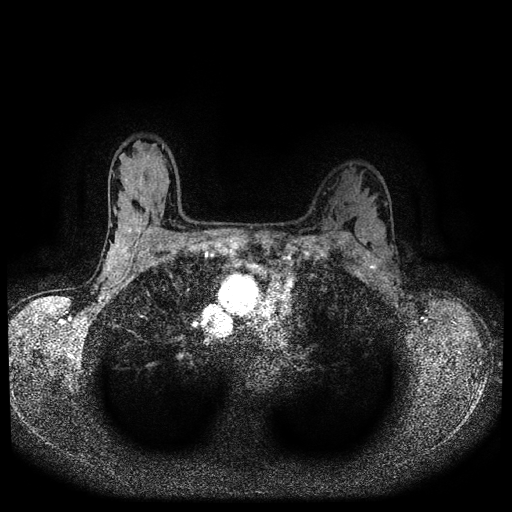
Breast MRI (dynamic contrast-enhanced, multi-phase), one axial slice. Position 74 of 116 along the scan axis. Dynamic contrast-enhanced series, time point 2 of 5 at this slice position (early post-contrast). 1.5 T. TE 2.7 ms, TR 5.4 ms. 2 mm slice thickness. 512 × 512 image matrix. Female patient, age 32 years.
Structures marked on this image (semi-automatically segmented with operator editing):
- breast lesion (labelled benign in the annotation): bounding box [x1, y1, x2, y2] px = [349, 190, 358, 202]